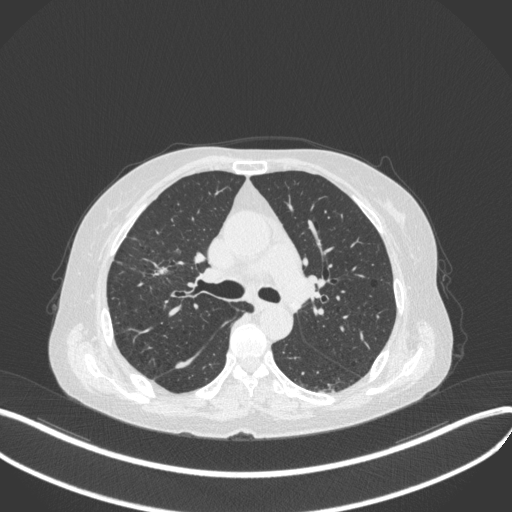
Chest CT, one axial slice; slice 257 of 429 in the series (ordered by position); 120 kVp; lung window (W 1500 / L -600 HU); 1 mm slice thickness; 512 × 512 image matrix, field of view 400 × 400 mm. Patient: female, 69 years. From the clinical record (not read from this slice): clinical TNM (as recorded): T1b N3 M0.
Outlined on this slice (bounding box drawn by a radiologist):
- lung tumour (recorded histology: small cell carcinoma): box from (x=144, y=249) to (x=181, y=286) px